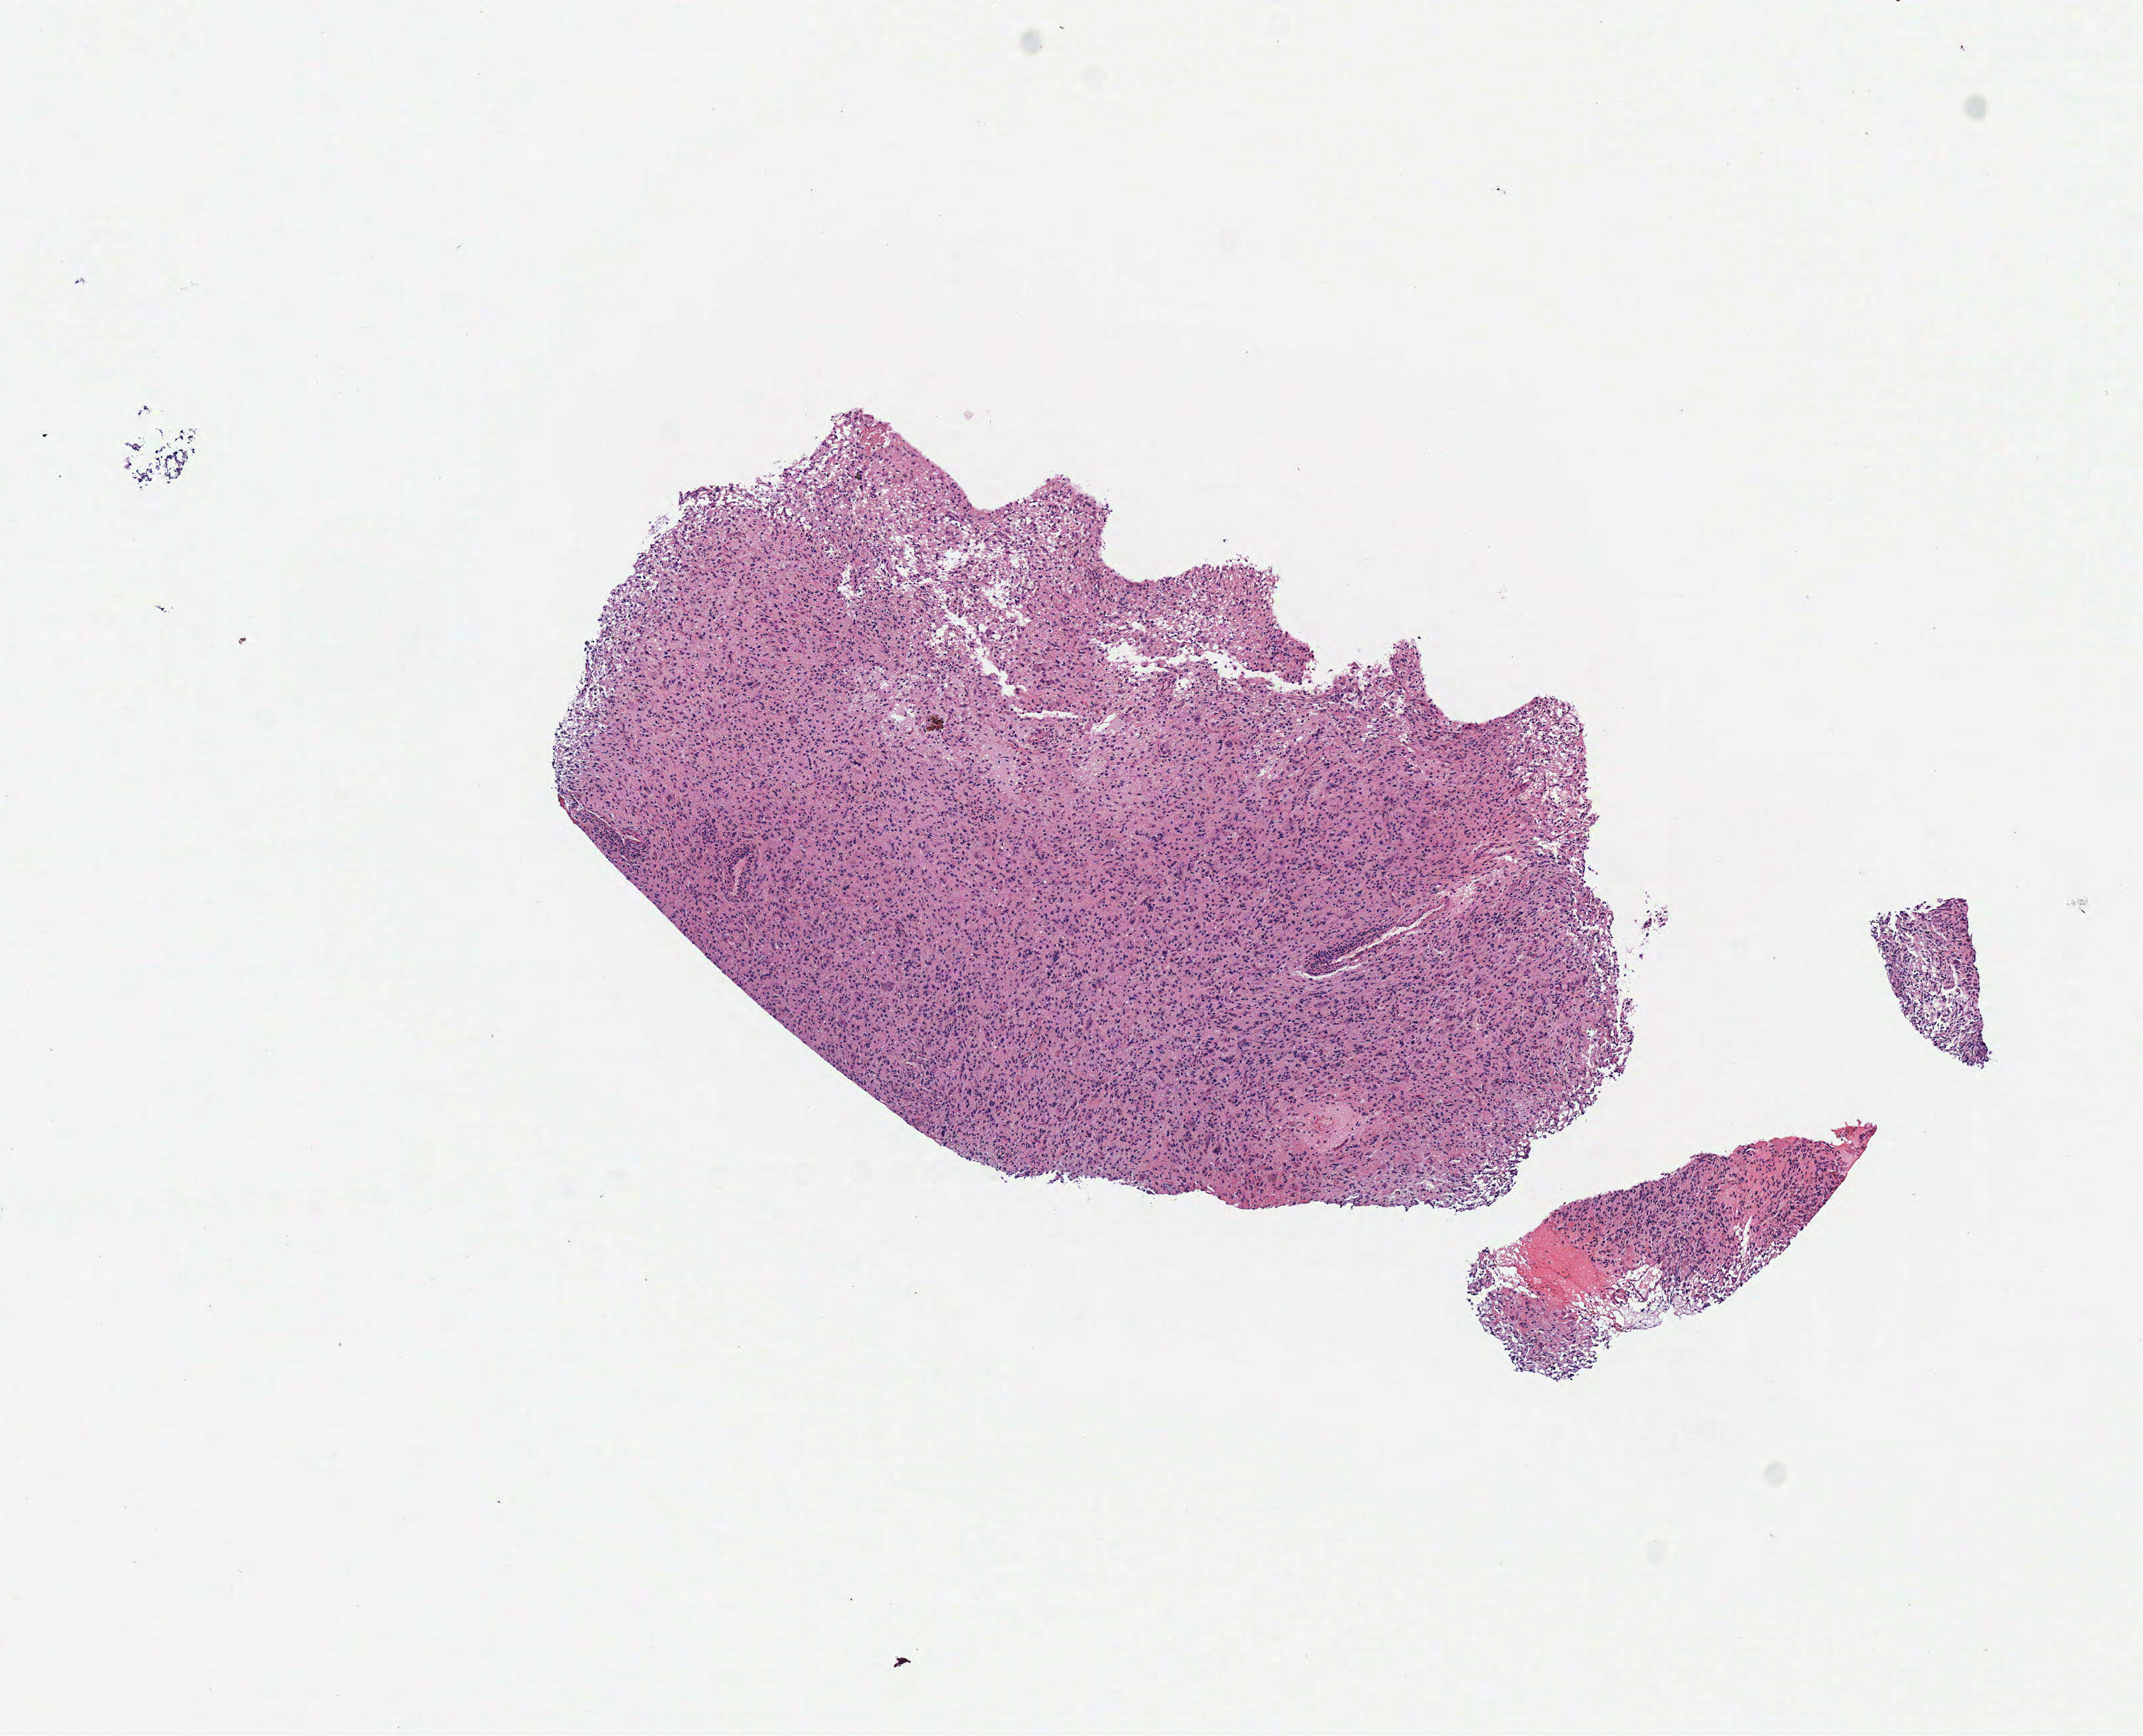
Digitized H&E tissue section (whole slide) — shown as a low-resolution overview of the whole scanned area (about 6.3 x 5.1 mm); frozen section from the top of the tissue portion; primary tumour sample from the colon. Male patient; age at initial diagnosis 58 years. Composition of this section per pathologist review: tumour cells 68%, tumour nuclei 80%, normal cells 0%, stromal cells 25%, necrosis 8%.
* AJCC pathologic stage: IIA (7th edition)
* diagnosis: Adenocarcinoma, NOS (sigmoid colon)
* lymph nodes positive (case pathology): 0 of 21 examined